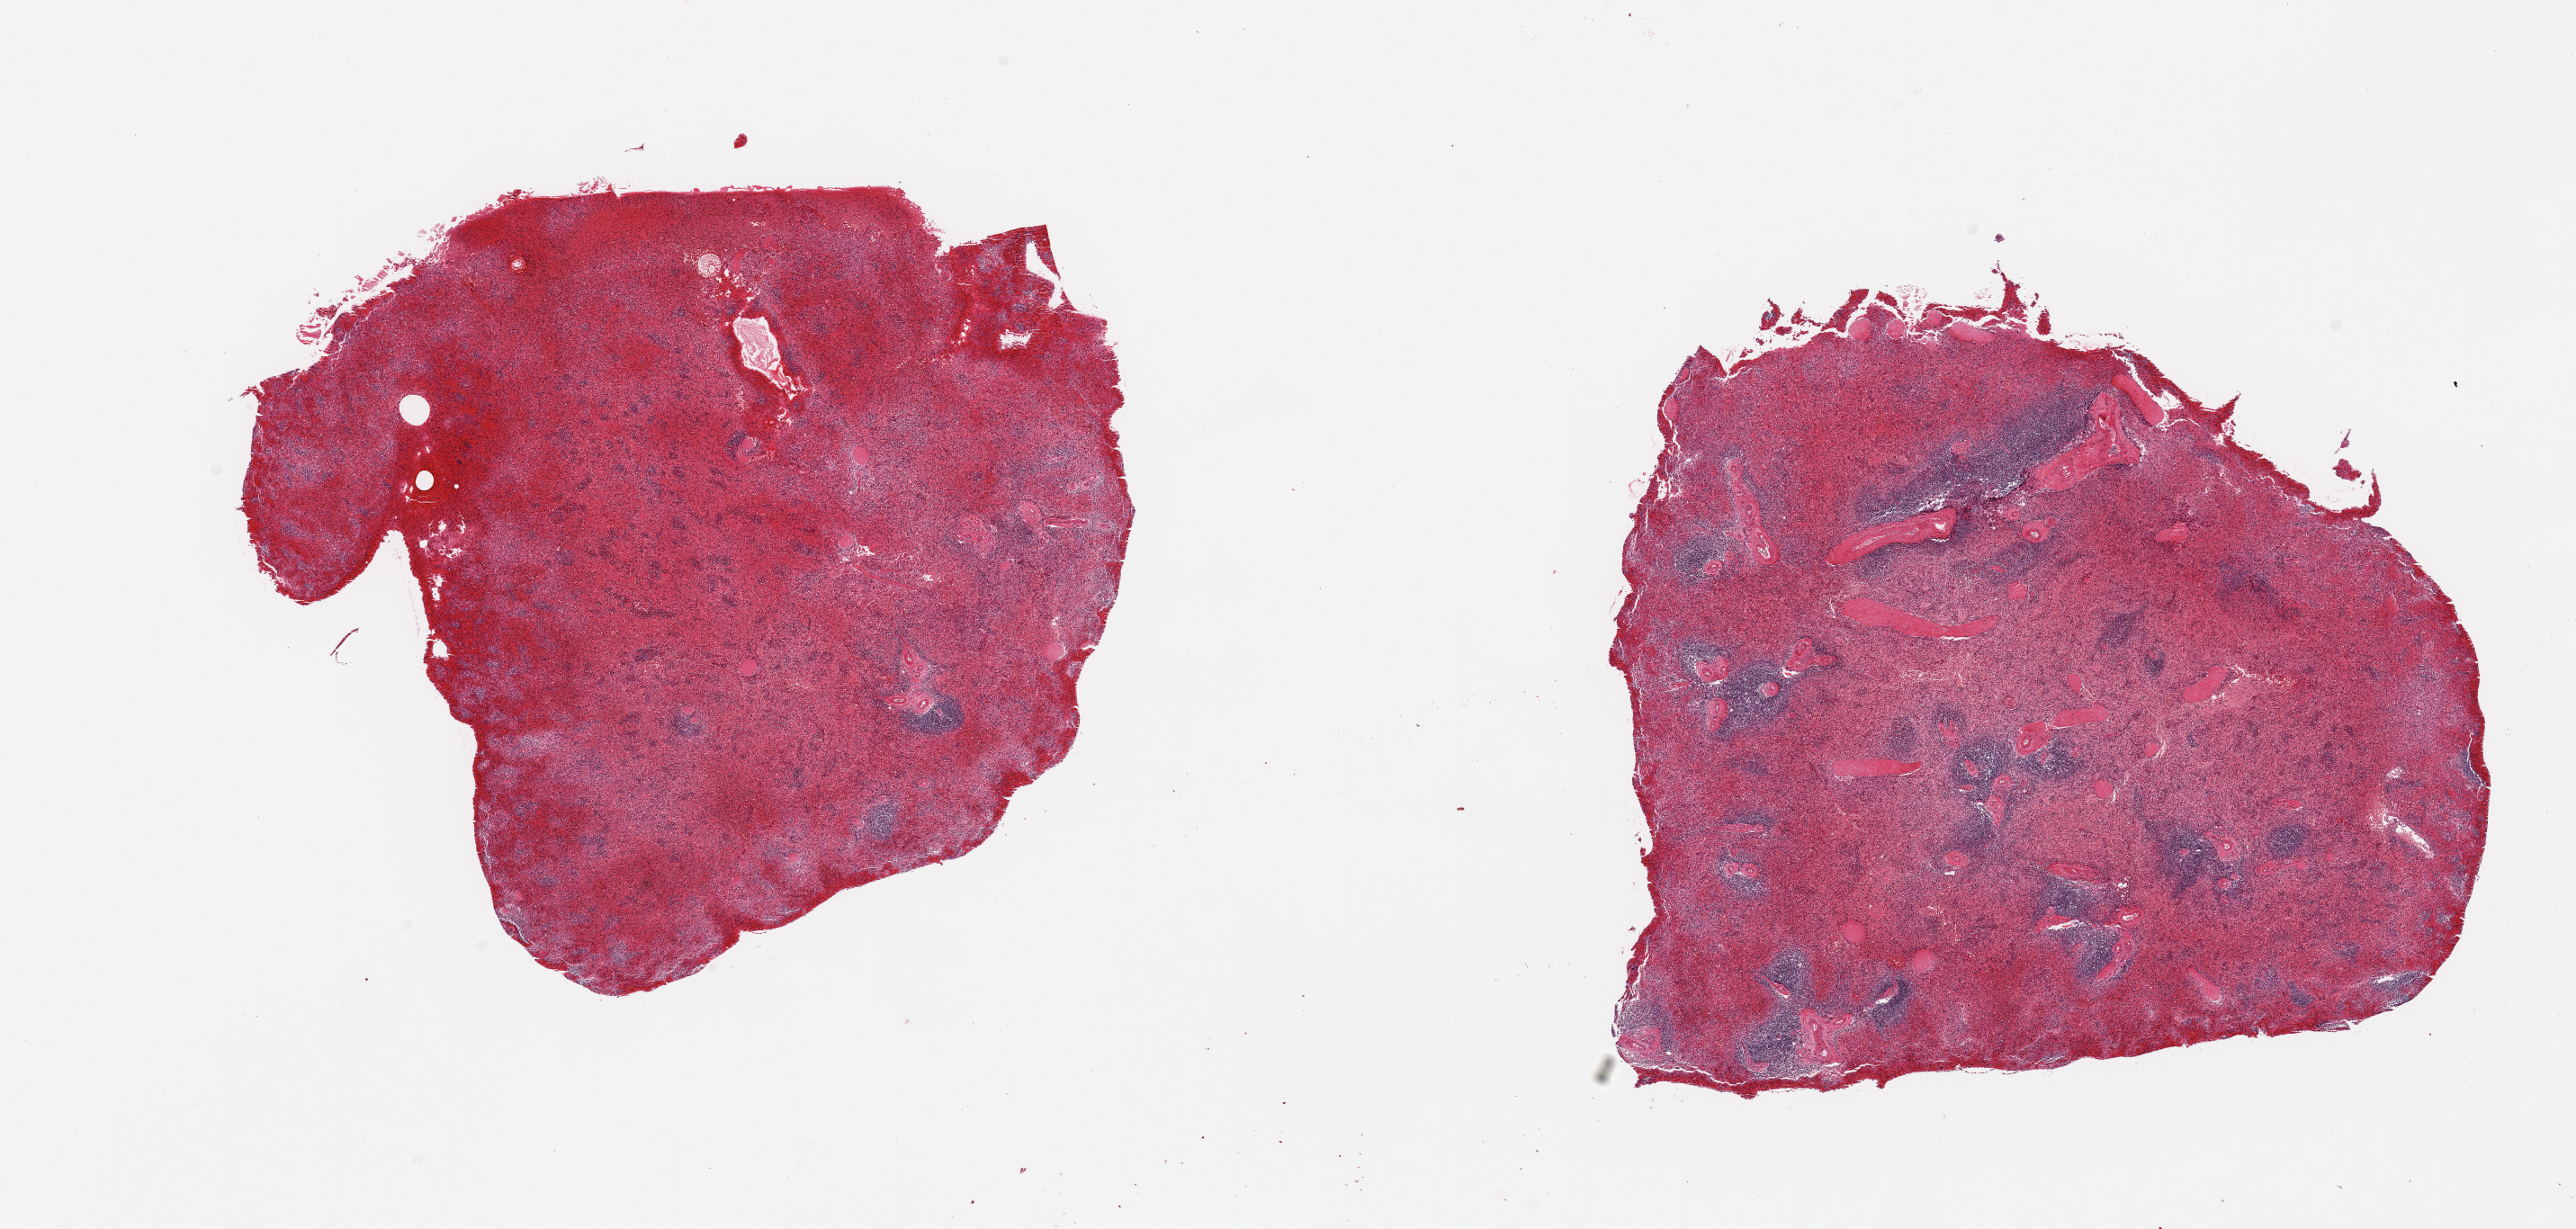
Hematoxylin and eosin (H&E) whole-slide image — a low-resolution overview of the entire scanned area, about 22.6 x 10.8 mm (acquisition: 20x scan); PAXgene-fixed, paraffin-embedded tissue; sampled site (target tissue): spleen; donor tissue sample. Donor sex: female.
- reviewer comment on this tissue sample: 2 pieces; severe congestion